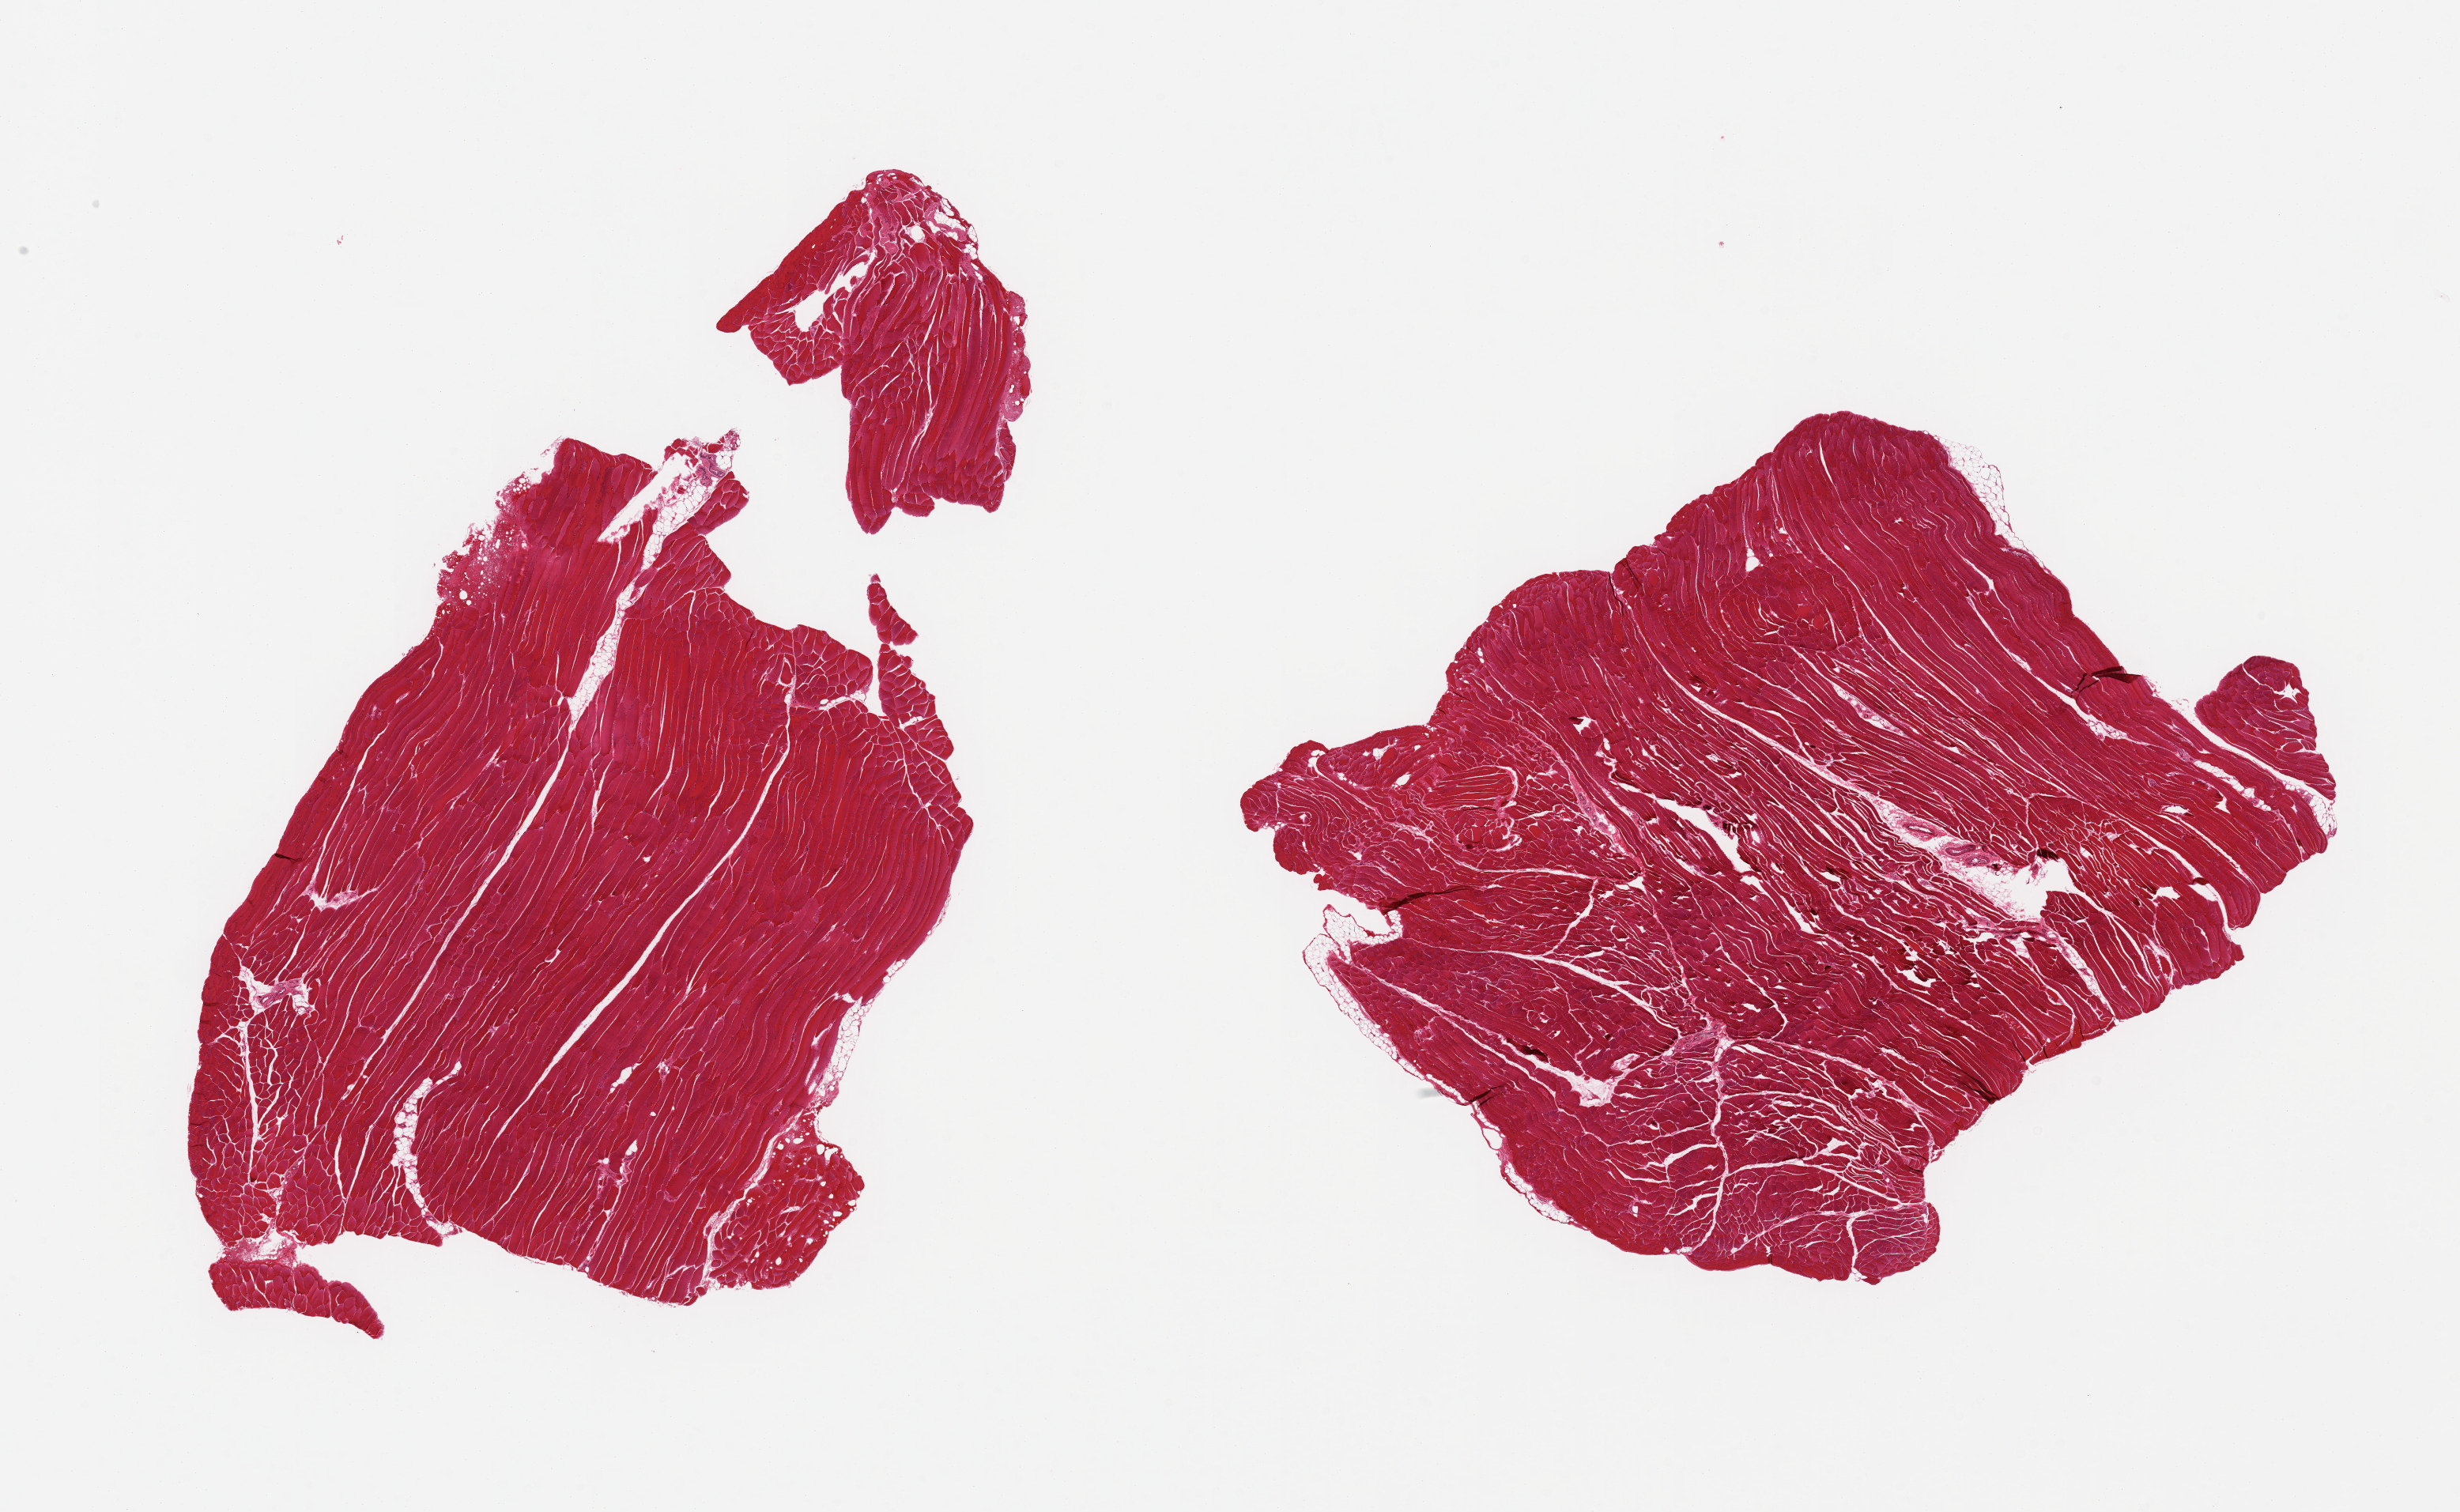
H&E whole-slide image, brightfield, shown as a low-resolution overview of the whole scanned area (about 24.6 x 15.1 mm, from a 20x scan). PAXgene-fixed paraffin-embedded (PFPE) section. Sampled site (target tissue): skeletal muscle. Donor tissue sample.
Reviewer comment on this tissue sample: 2 pieces; minimal internal fat.